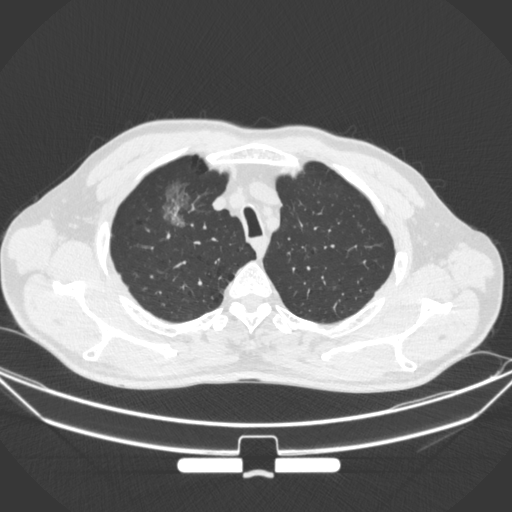
Chest CT, one axial slice. Slice 287 of 355 in the series (ordered by position). 120 kVp. Lung window (W 1500 / L -600 HU). 512 × 512 image matrix, field of view 399 × 399 mm. Patient: male, 67 years. From the clinical record (not read from this slice): clinical TNM (as recorded): T1c N0 M0; histopathological grade: G2.
Annotated regions visible in this slice (bounding box drawn by a radiologist):
- lung tumour (recorded histology: adenocarcinoma): bounding box (x1, y1, x2, y2) in pixels: (157, 177, 196, 227)